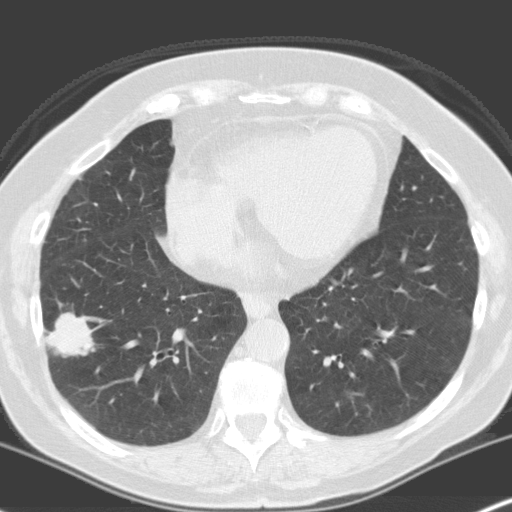
Low-dose screening chest CT, one axial slice. Slice 66 of 160 in the series (ordered by position). Lung window (W 1500 / L -600 HU). 512 × 512 image matrix.
Structures marked on this image (expert manual segmentation):
- lesion 1 (tumor, lower lobe of right lung): bounding box <47,312,95,358> (left, top, right, bottom; pixels)